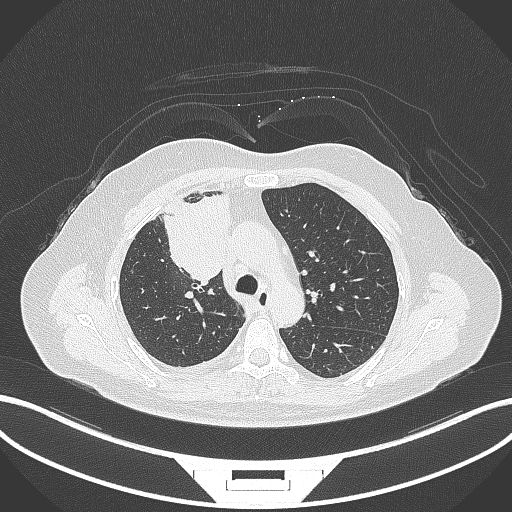
Chest CT, one axial slice. Position 201 of 305 along the scan axis. Lung window (W 1500 / L -600 HU). 1 mm slice thickness. 512 × 512 image matrix. Patient: female, 52 years. Case-level facts recorded for this patient, not image findings: clinical TNM (as recorded): T3 N1 M1.
Annotated regions visible in this slice (rectangle marked by the reading radiologist):
- lung tumour (recorded histology: adenocarcinoma): bounding box <159,190,231,287> (left, top, right, bottom; pixels)